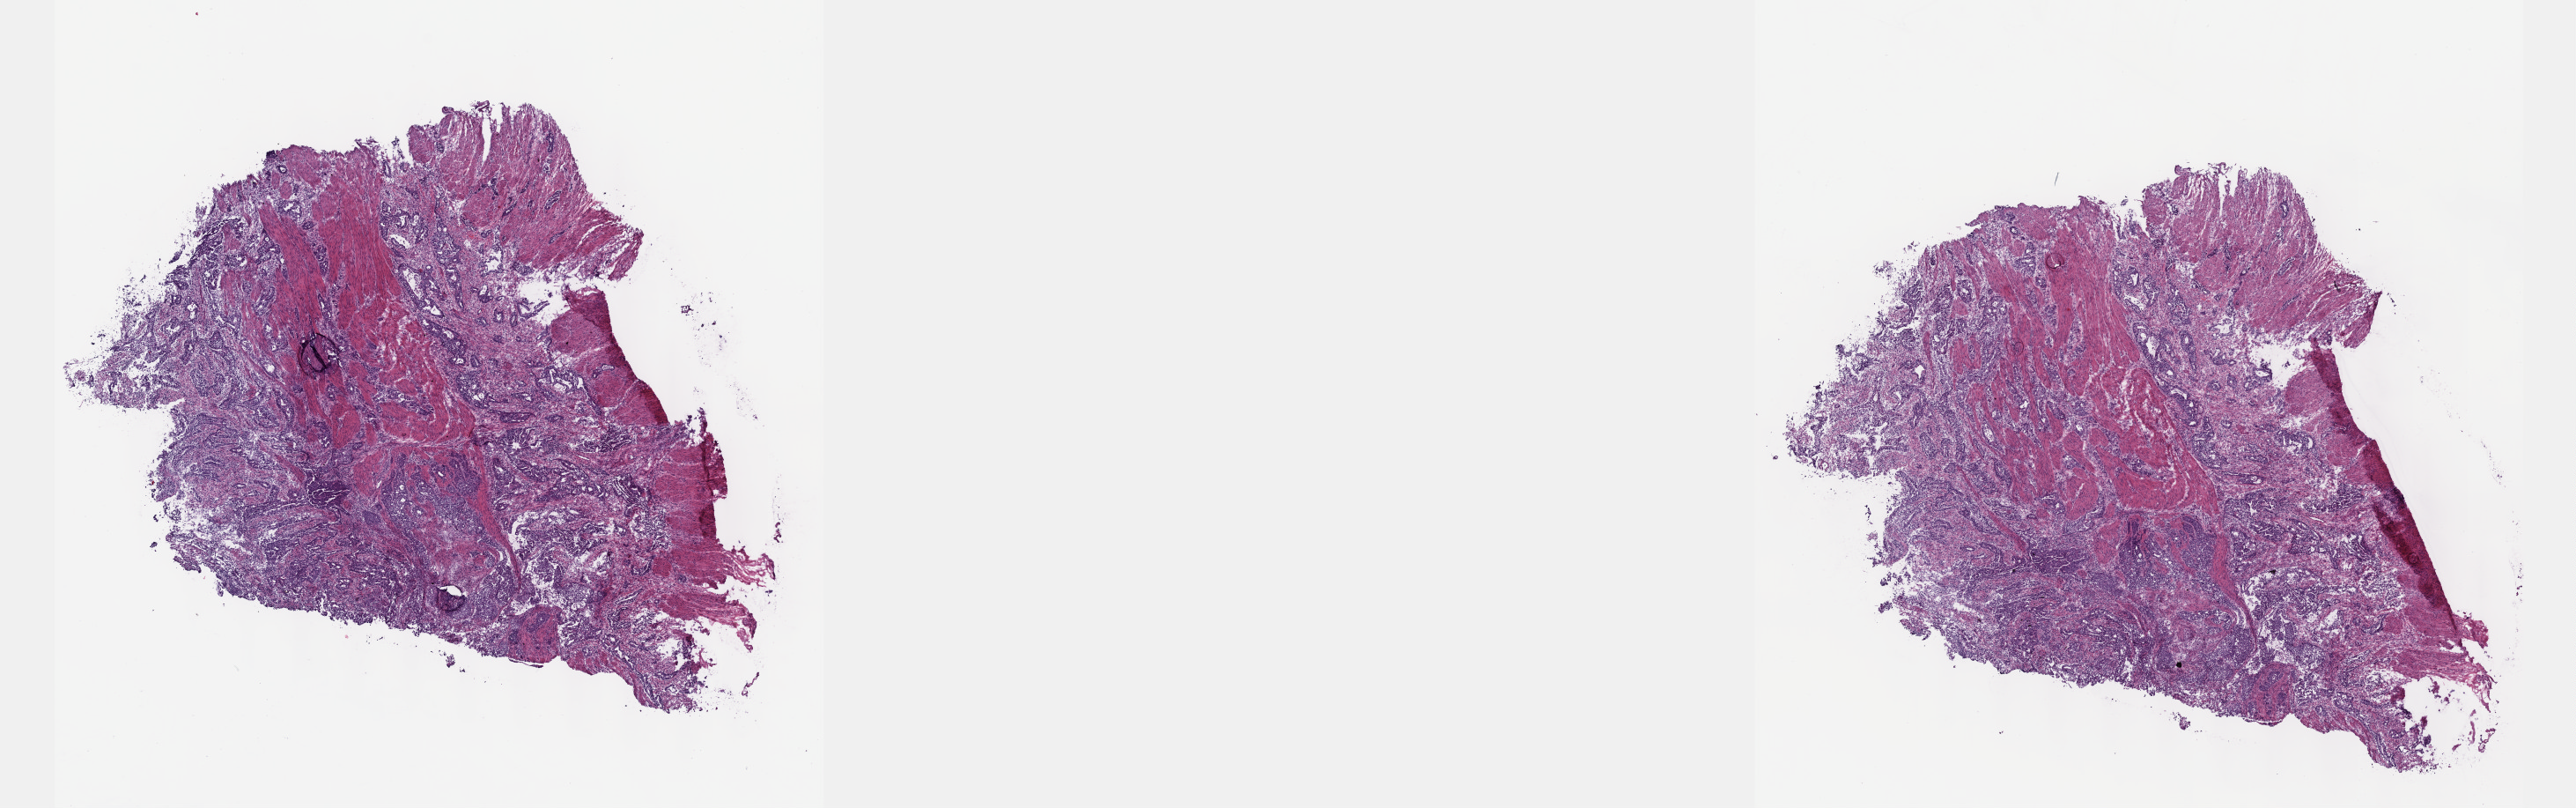
H&E-stained whole-slide image — shown as a low-resolution overview of the whole scanned area (about 23.6 x 7.4 mm, acquisition: 40x scan), frozen section, sample: primary tumour, esophagus. Patient: male, age at initial diagnosis 76 years. Histologic grade: GX (grade cannot be assessed). Pathologist review of this section (percent, as recorded): tumour cells 100%, tumour nuclei 60%, normal cells 0%, stromal cells 0%, necrosis 0%. Infiltration values recorded for this section: lymphocyte infiltration 4%, monocyte infiltration 0%, neutrophil infiltration 0%.
Pathologic diagnosis: Adenocarcinoma, NOS. AJCC pathologic stage: IIB (5th edition). Lymph nodes positive (case pathology): 0 of 3 examined. TNM: T3 N0 M0.